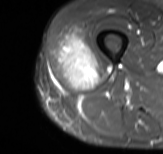
MRI of an extremity soft-tissue mass, one axial slice. STIR. MR volume resampled by the dataset authors to the PET/CT grid (not the native acquisition matrix). 163 × 154 image matrix, field of view 159 × 150 mm. Male patient. Case-level facts recorded for this patient, not image findings: histological type: poorly differentiated synovial sarcoma; grade: high; site of the primary tumour: right buttock.
Outlined on this slice (expert contour drawn on MRI and transferred to this co-registered scan by the dataset authors):
- gross tumour volume including surrounding oedema: box from (x=57, y=32) to (x=108, y=90) px
- gross tumour volume (mass): (x=59, y=36)–(x=97, y=88)